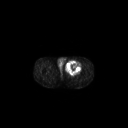
FDG PET of an extremity soft-tissue mass (from a PET/CT study), one axial slice; position 253 of 267 along the scan axis; 3.27 mm slice thickness; 128 × 128 image matrix. Male patient, age 63 years. From the clinical record (not read from this slice): histological type: pleiomorphic liposarcoma; grade: high; site of the primary tumour: left thigh.
Outlined on this slice (expert contour drawn on MRI and transferred to this co-registered scan by the dataset authors):
- gross tumour volume including surrounding oedema: bounding box <65,60,82,74> (left, top, right, bottom; pixels)
- gross tumour volume (mass): <65,60,81,74>